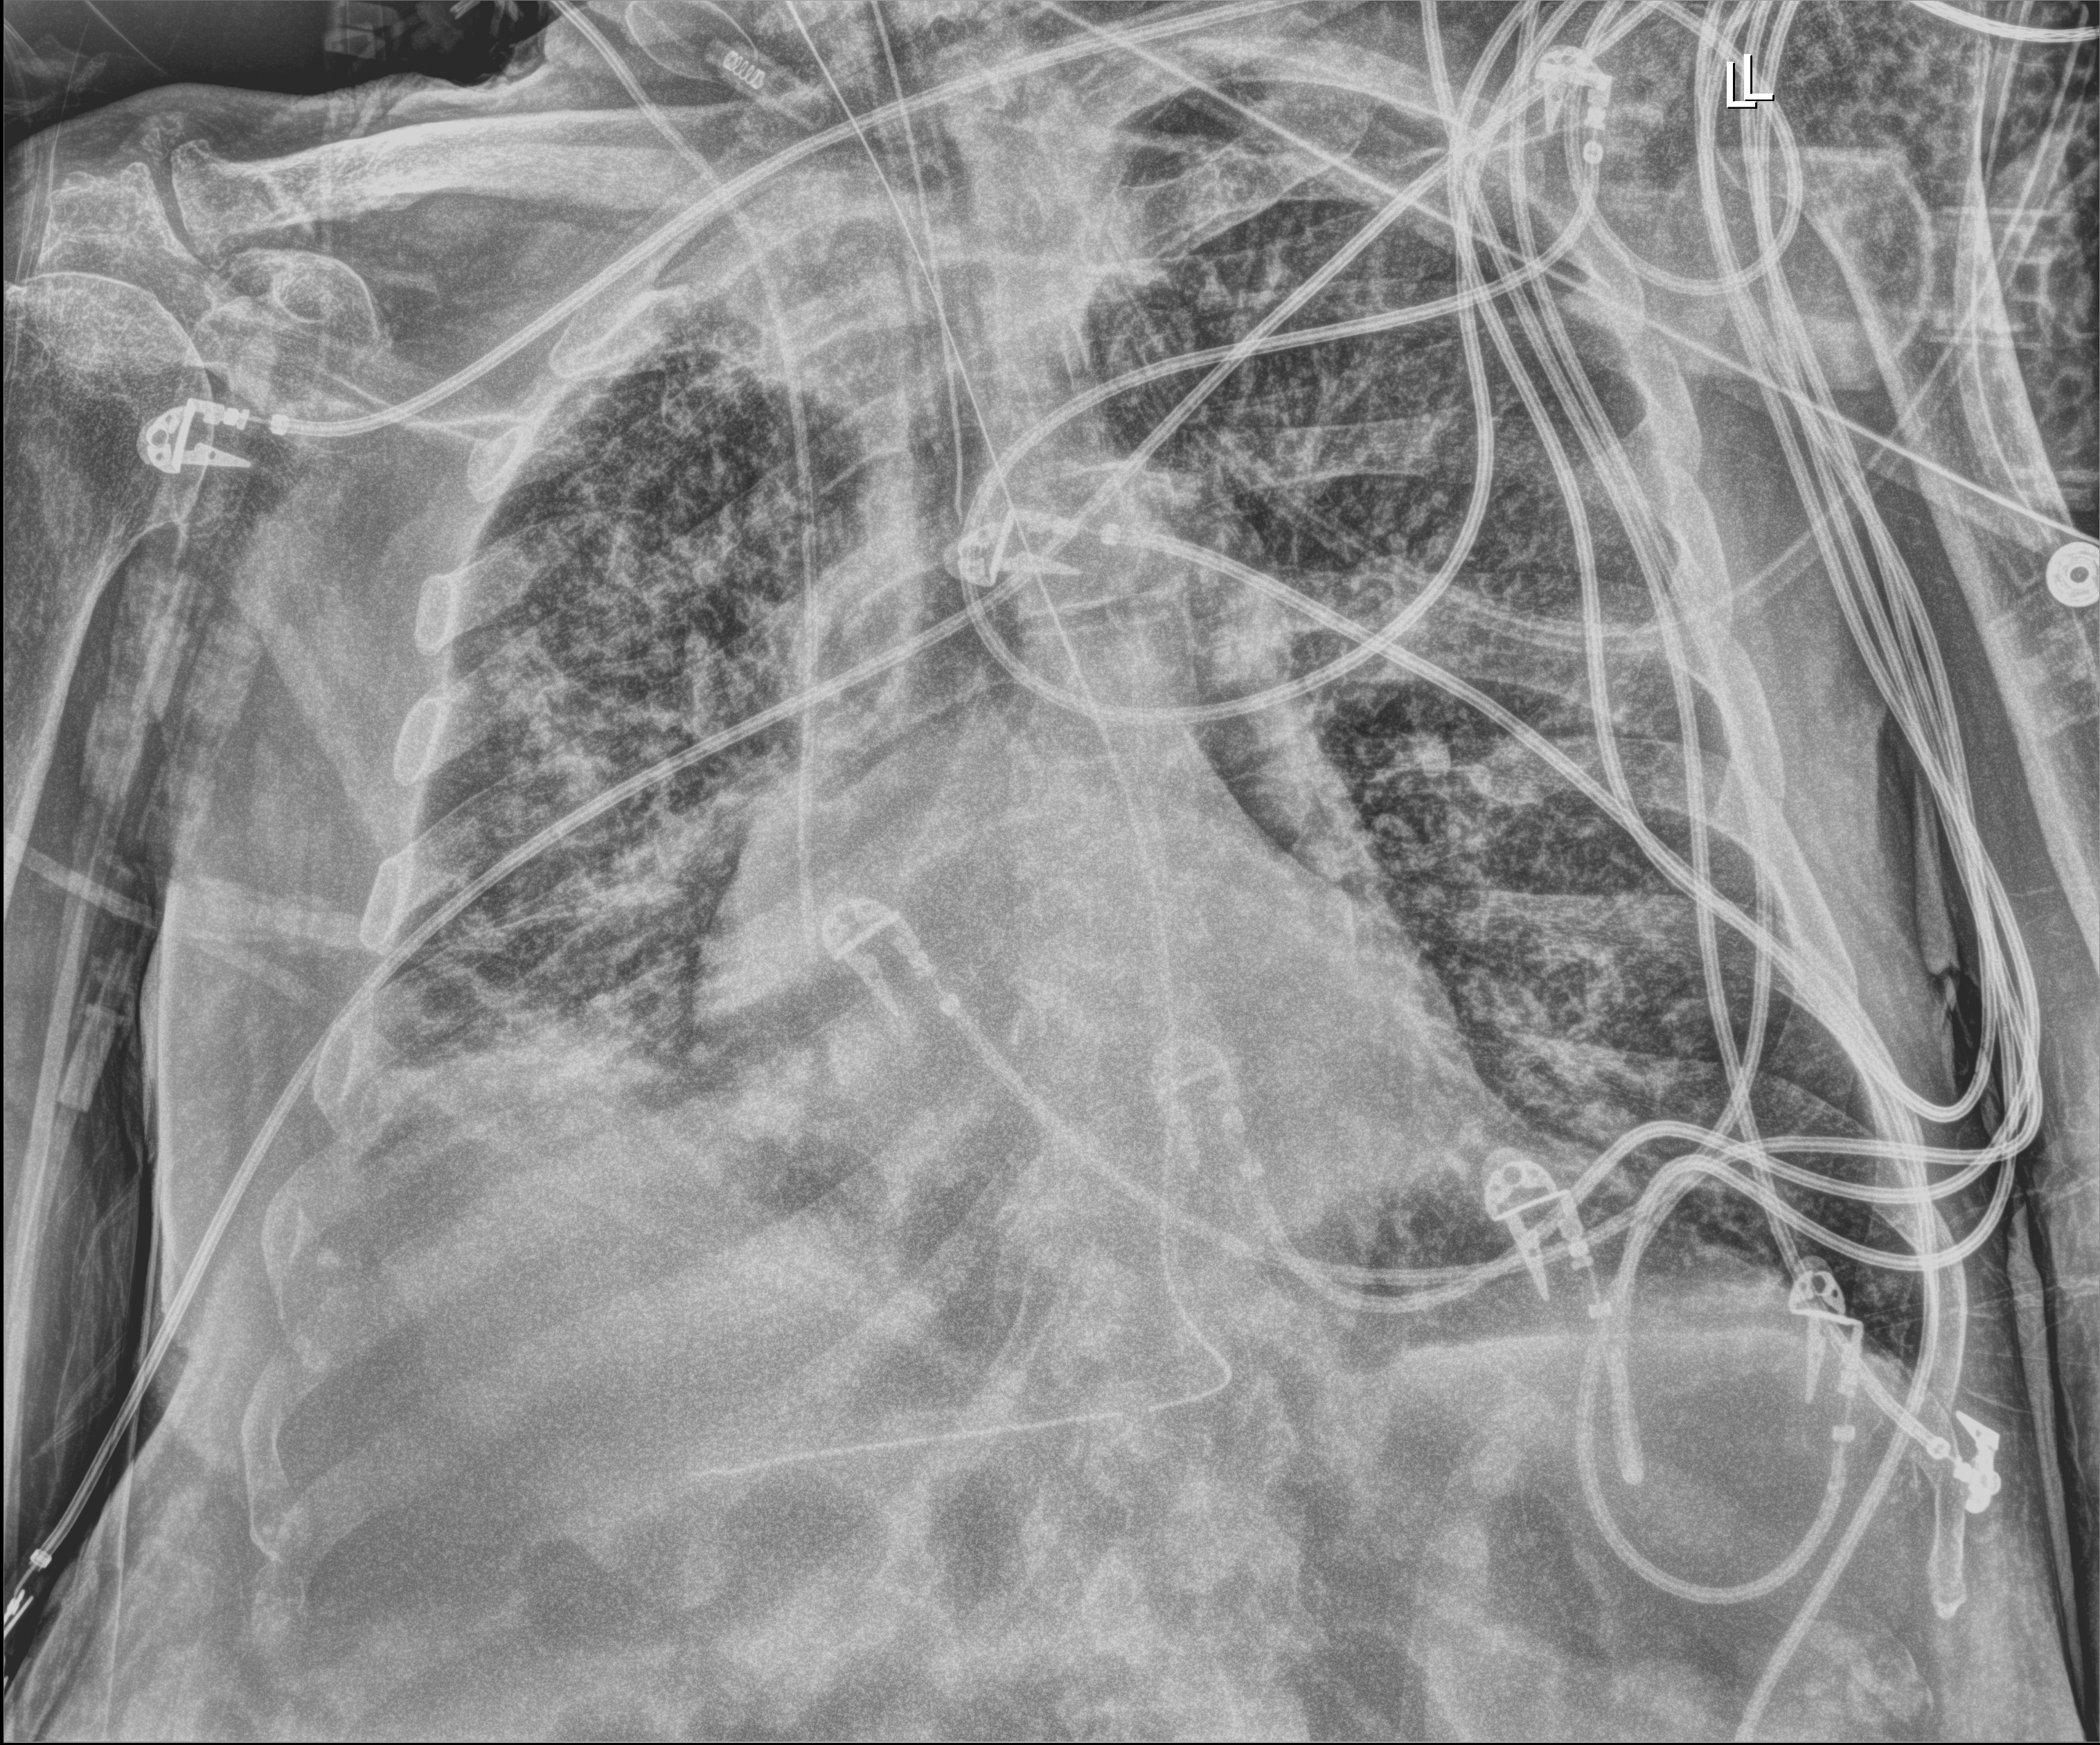
Portable chest radiograph, anteroposterior (AP) projection. Male patient hospitalised with COVID-19, age 75–90 years.
From the hospital-stay record, not from the radiograph (when in the stay this image was taken is not recorded): mechanically ventilated during this hospital stay: yes; length of hospital stay: 28 days.